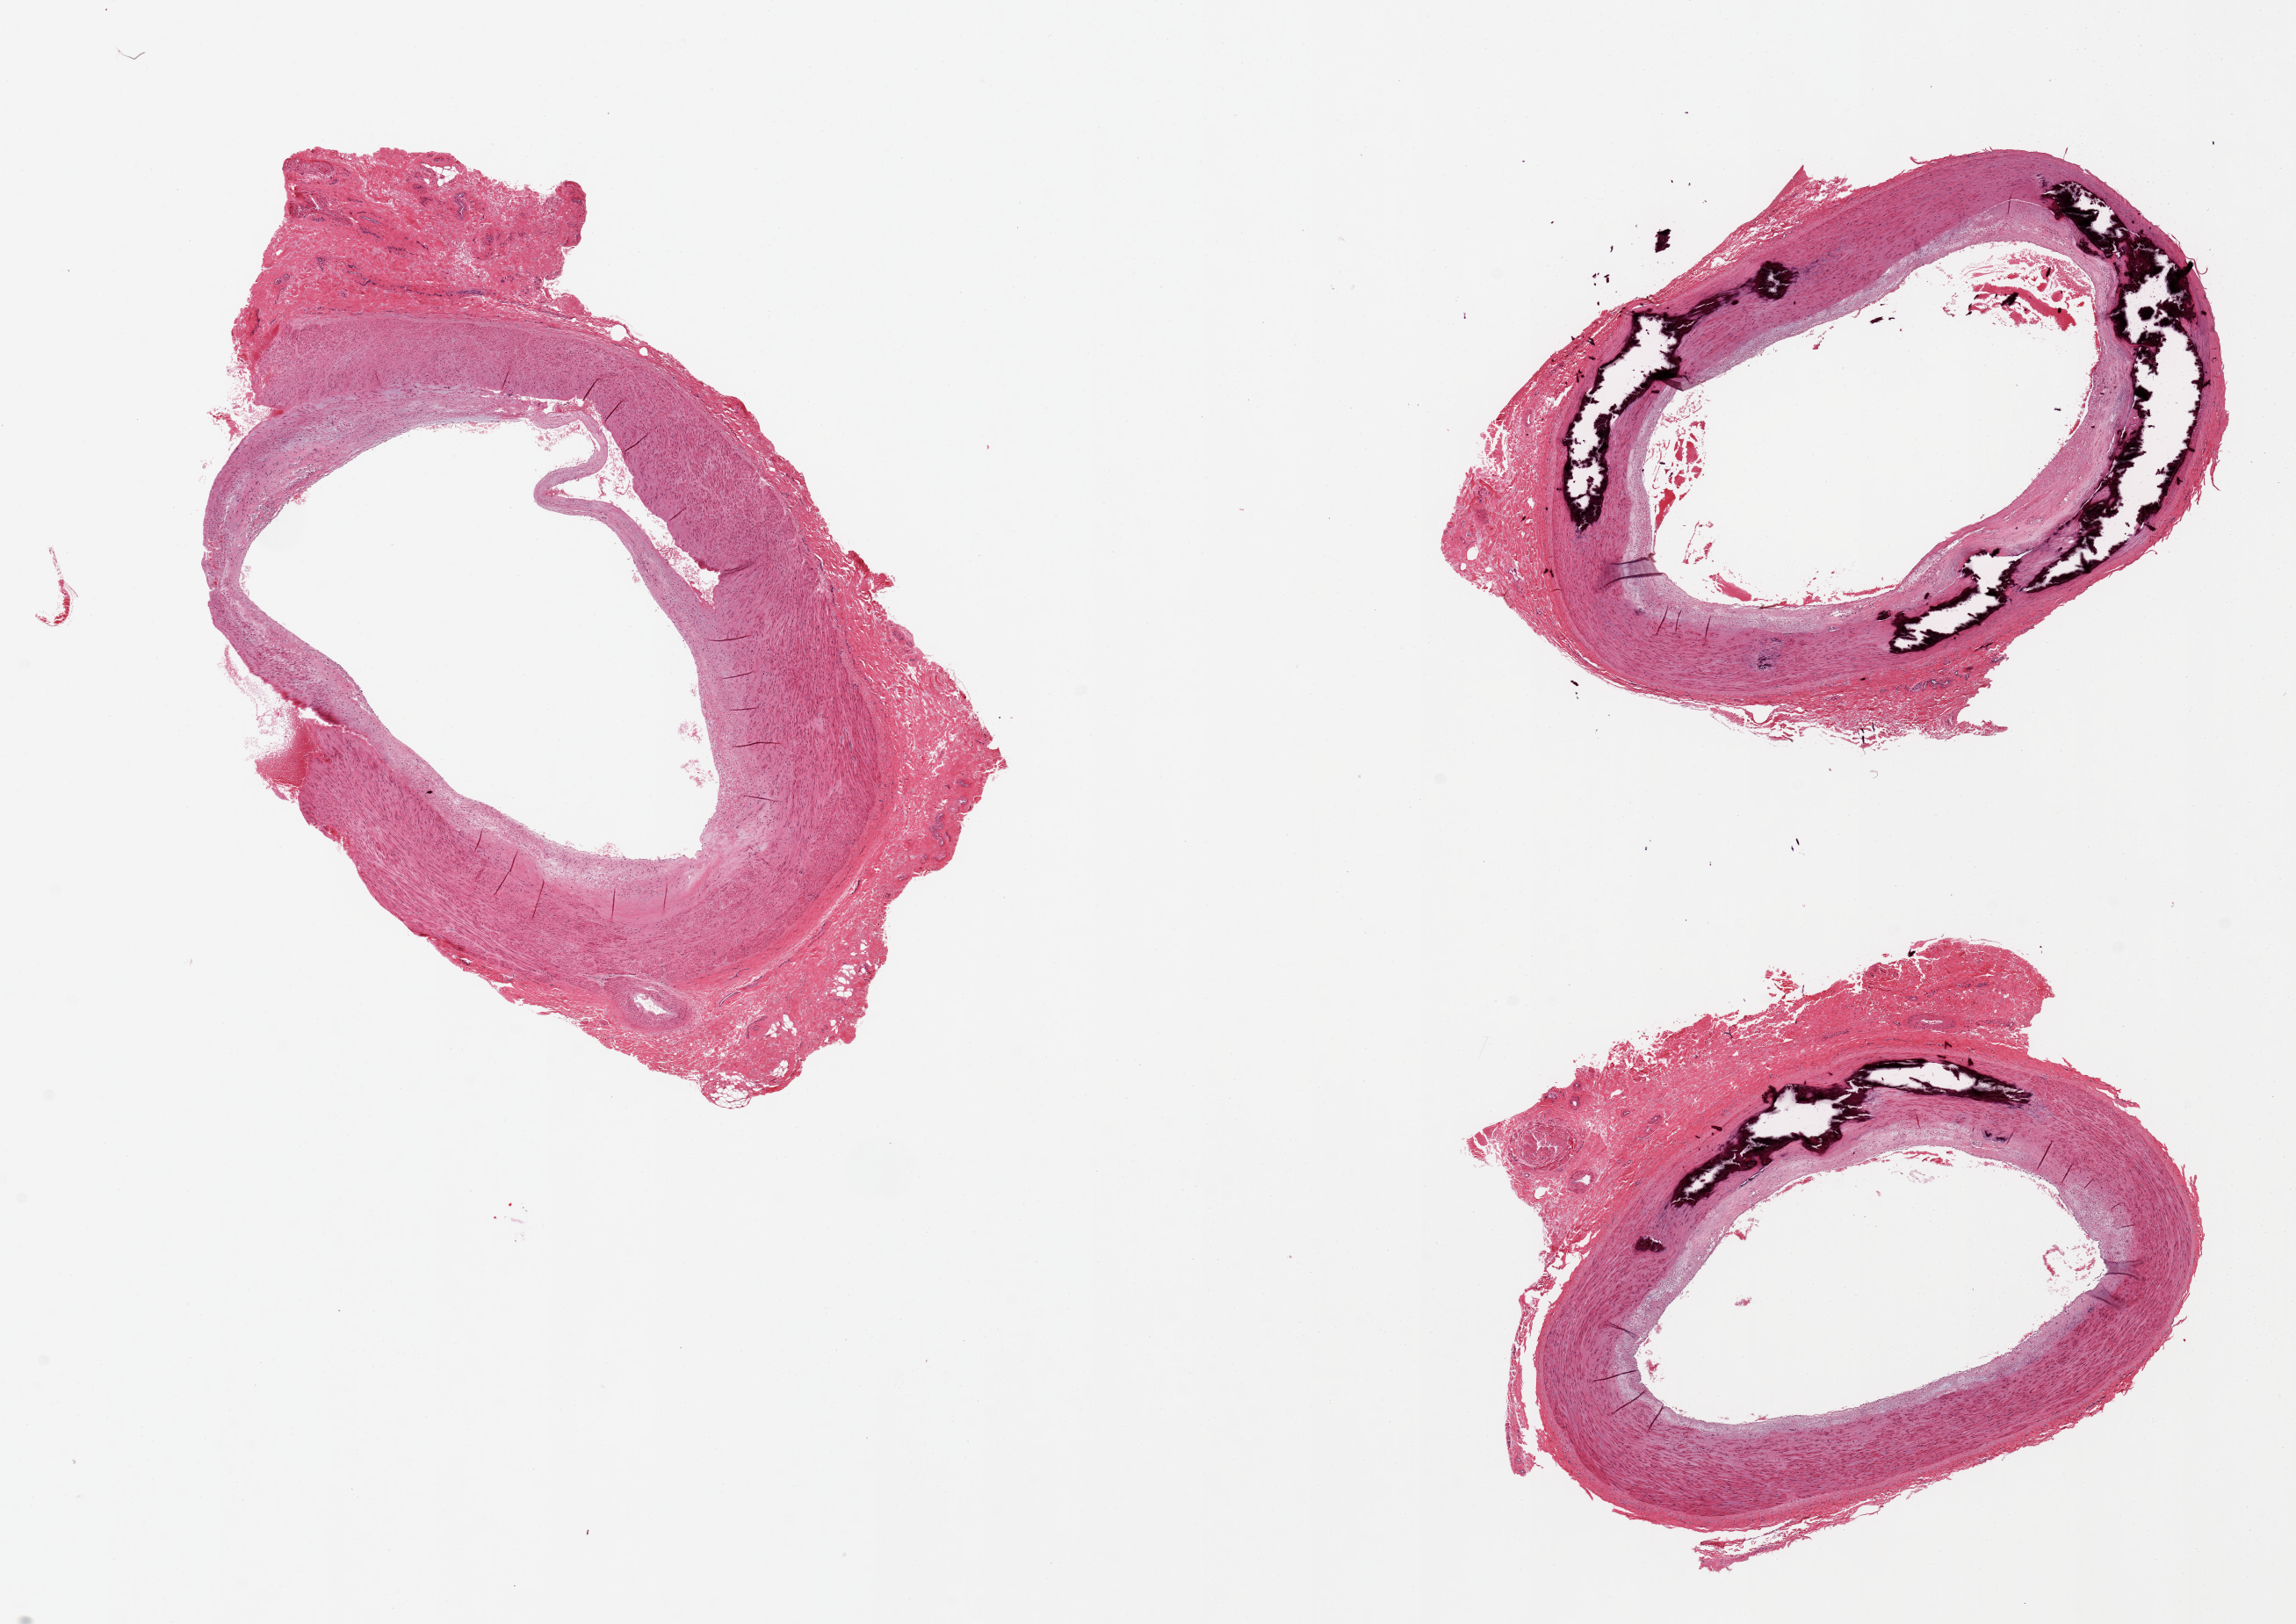
Digitized H&E-stained section, brightfield, a low-resolution overview of the entire scanned area, about 20.7 x 14.6 mm. PAXgene-fixed paraffin-embedded (PFPE) section. Section of tibial artery (target tissue). Donor tissue sample. Donor sex: male.
• reviewer comment on this tissue sample: 3 pieces, 2 with extensive medial calcification (Monckeberg sclerosis)